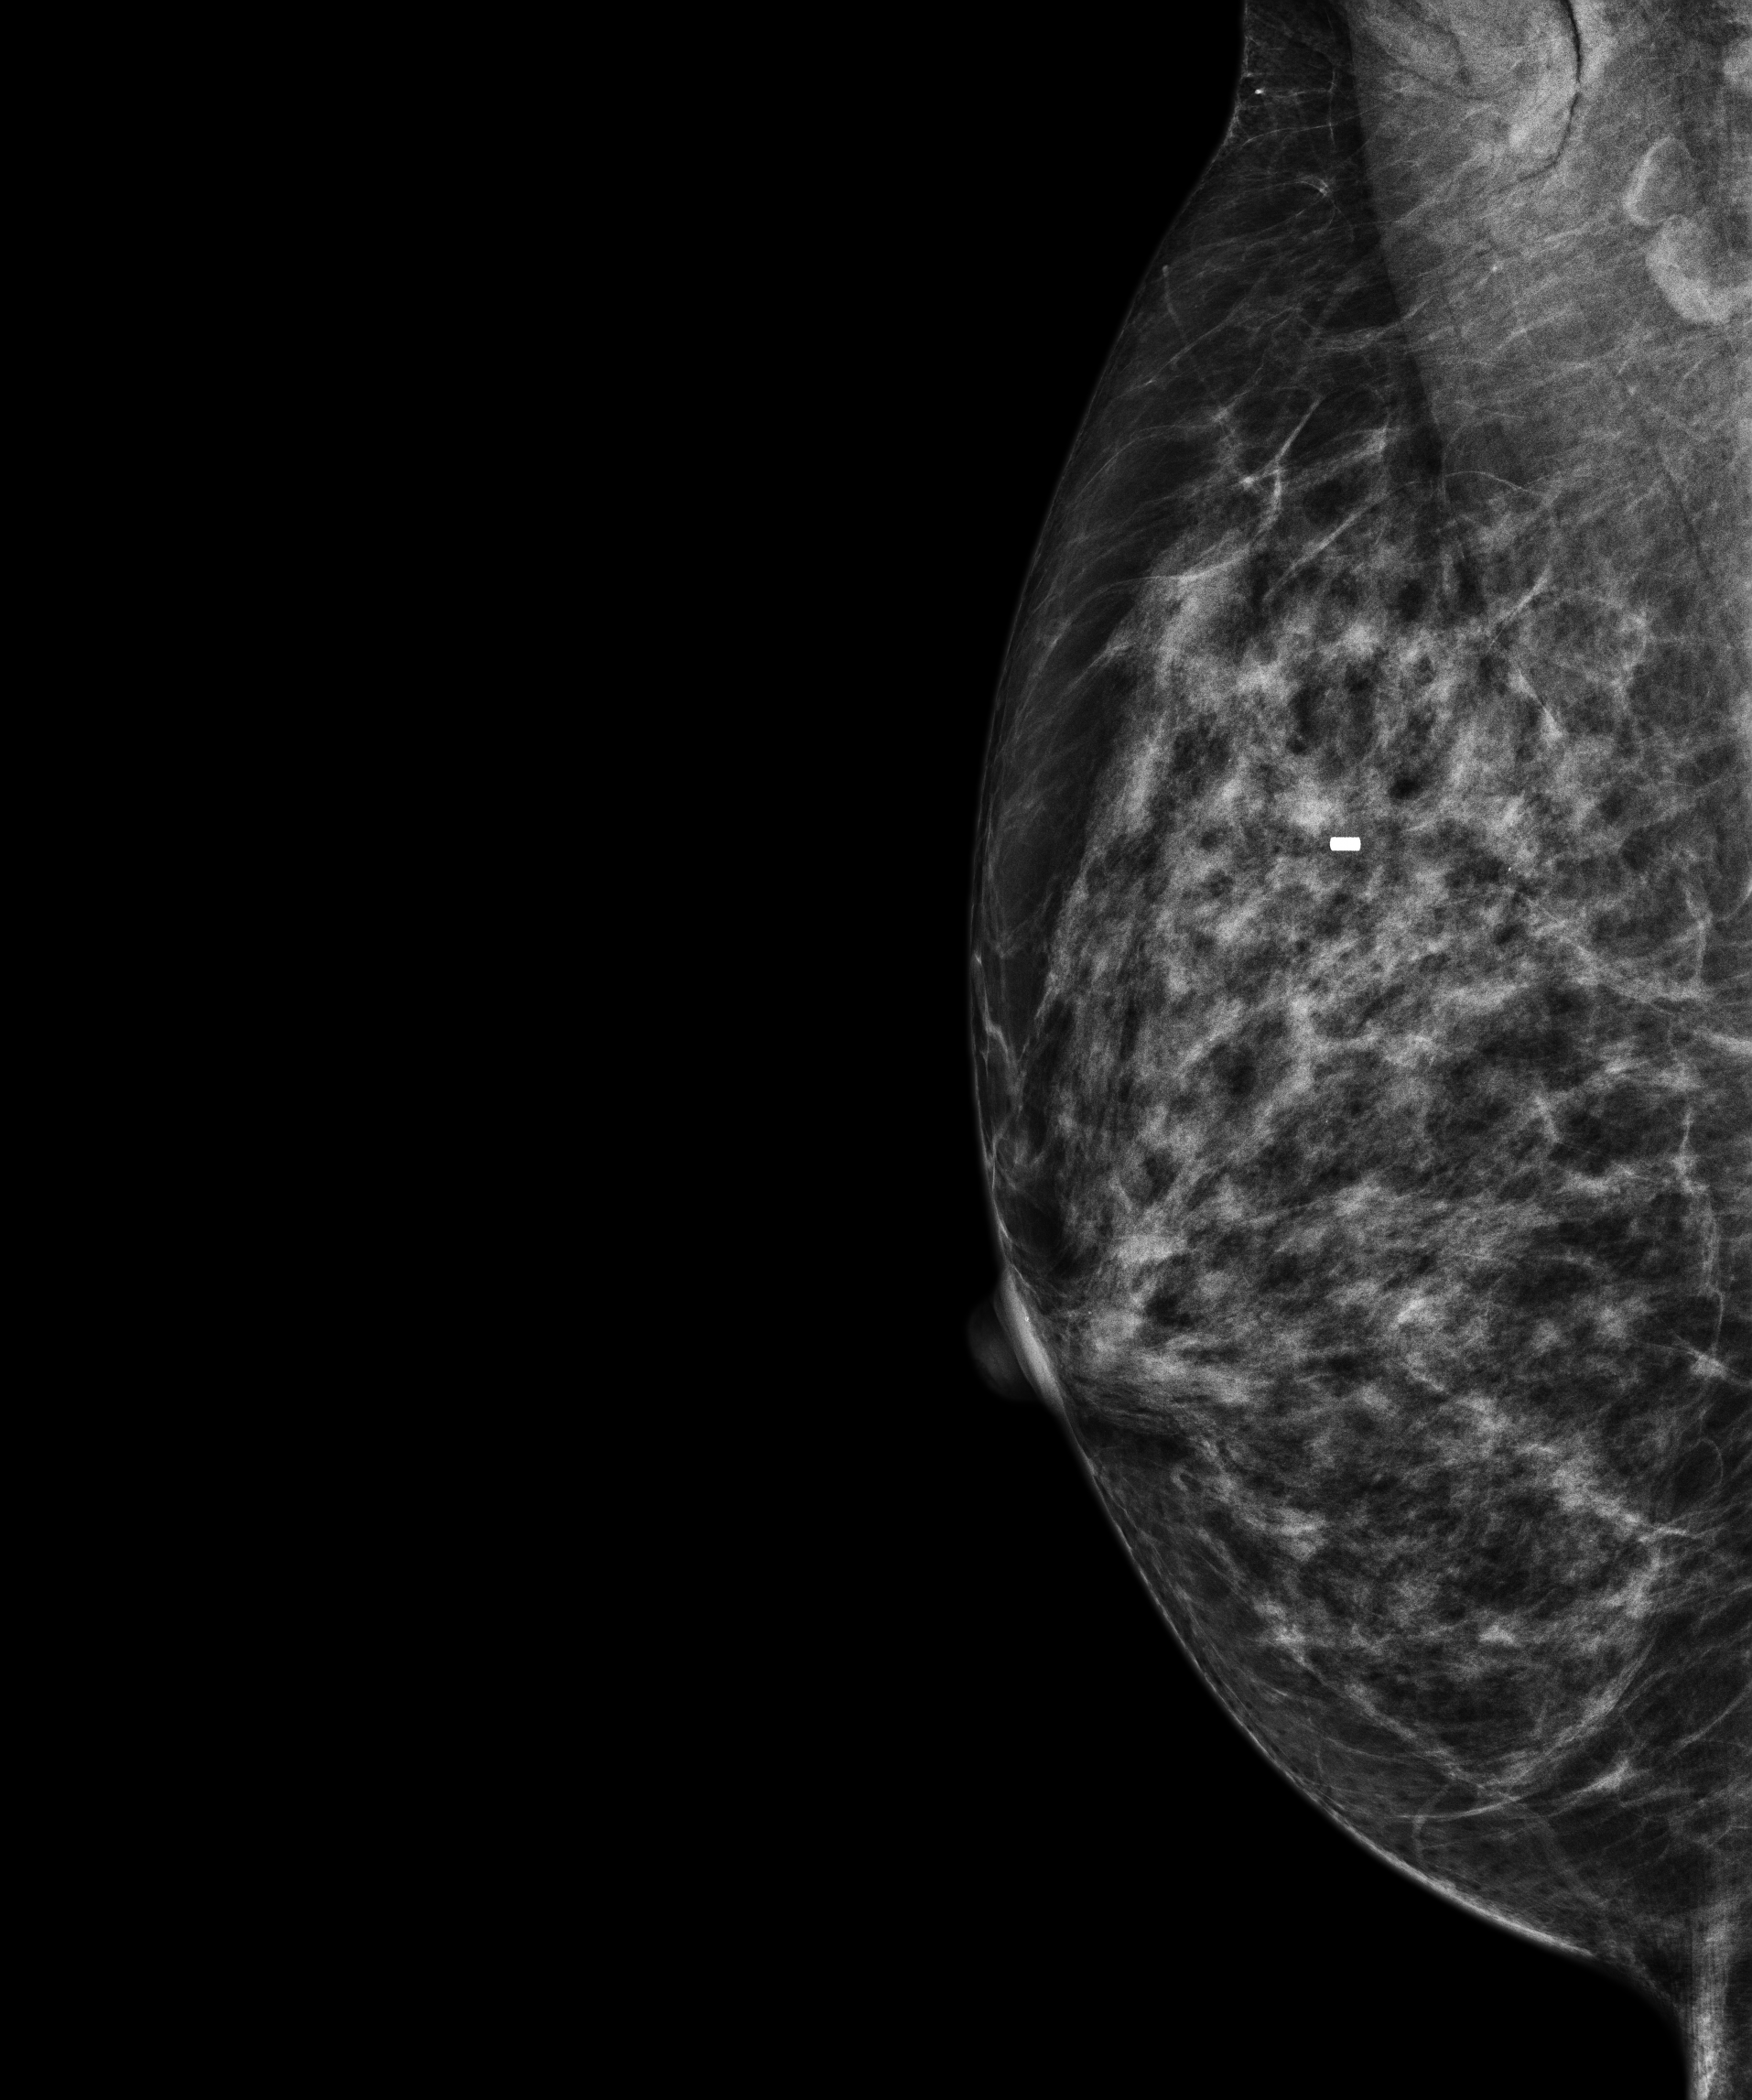
Screening examination; compressed breast thickness 43.4 mm. Patient: female, 57 years.
Image type: full-field digital mammogram. Breast: right. Projection: MLO view.